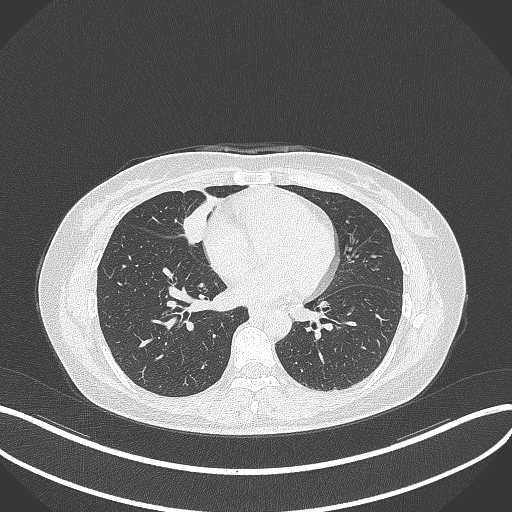
Chest CT, one axial slice; position 117 of 284 along the scan axis; 120 kVp; lung window (W 1500 / L -600 HU); 512 × 512 image matrix, field of view 400 × 400 mm. Female patient, age 43 years. From the clinical record (not read from this slice): clinical TNM (as recorded): T1c N3 M1.
Annotated regions visible in this slice (rectangle marked by the reading radiologist):
- lung tumour (recorded histology: adenocarcinoma): box from (x=180, y=200) to (x=208, y=247) px